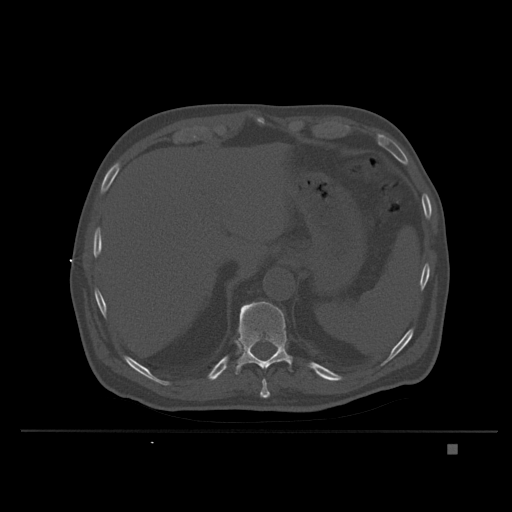
CT including the spine, one axial slice; position 179 of 435 along the scan axis; bone window (W 1800 / L 400 HU); 1.5 mm slice thickness; 512 × 512 image matrix, field of view 434 × 434 mm. Patient: male, 73 years. Case-level facts recorded for this patient, not image findings: primary cancer: skin.
Structures marked on this image (semi-automatically segmented with operator editing):
- T10 vertebra: bounding box <260,379,270,398> (left, top, right, bottom; pixels)
- T11 vertebra: <235,301,293,375>